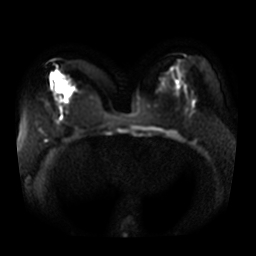
Breast MRI, one axial slice; position 16 of 36 along the scan axis; diffusion-weighted series; image 2 of 4 stored at this slice position (different b-values; order by instance number); 3 T; 5 mm slice thickness; 256 × 256 image matrix, field of view 370 × 370 mm. Female patient.
Annotated regions visible in this slice (manually delineated by an expert):
- tumour on diffusion-weighted imaging: bounding box (x1, y1, x2, y2) in pixels: (53, 73, 66, 102)